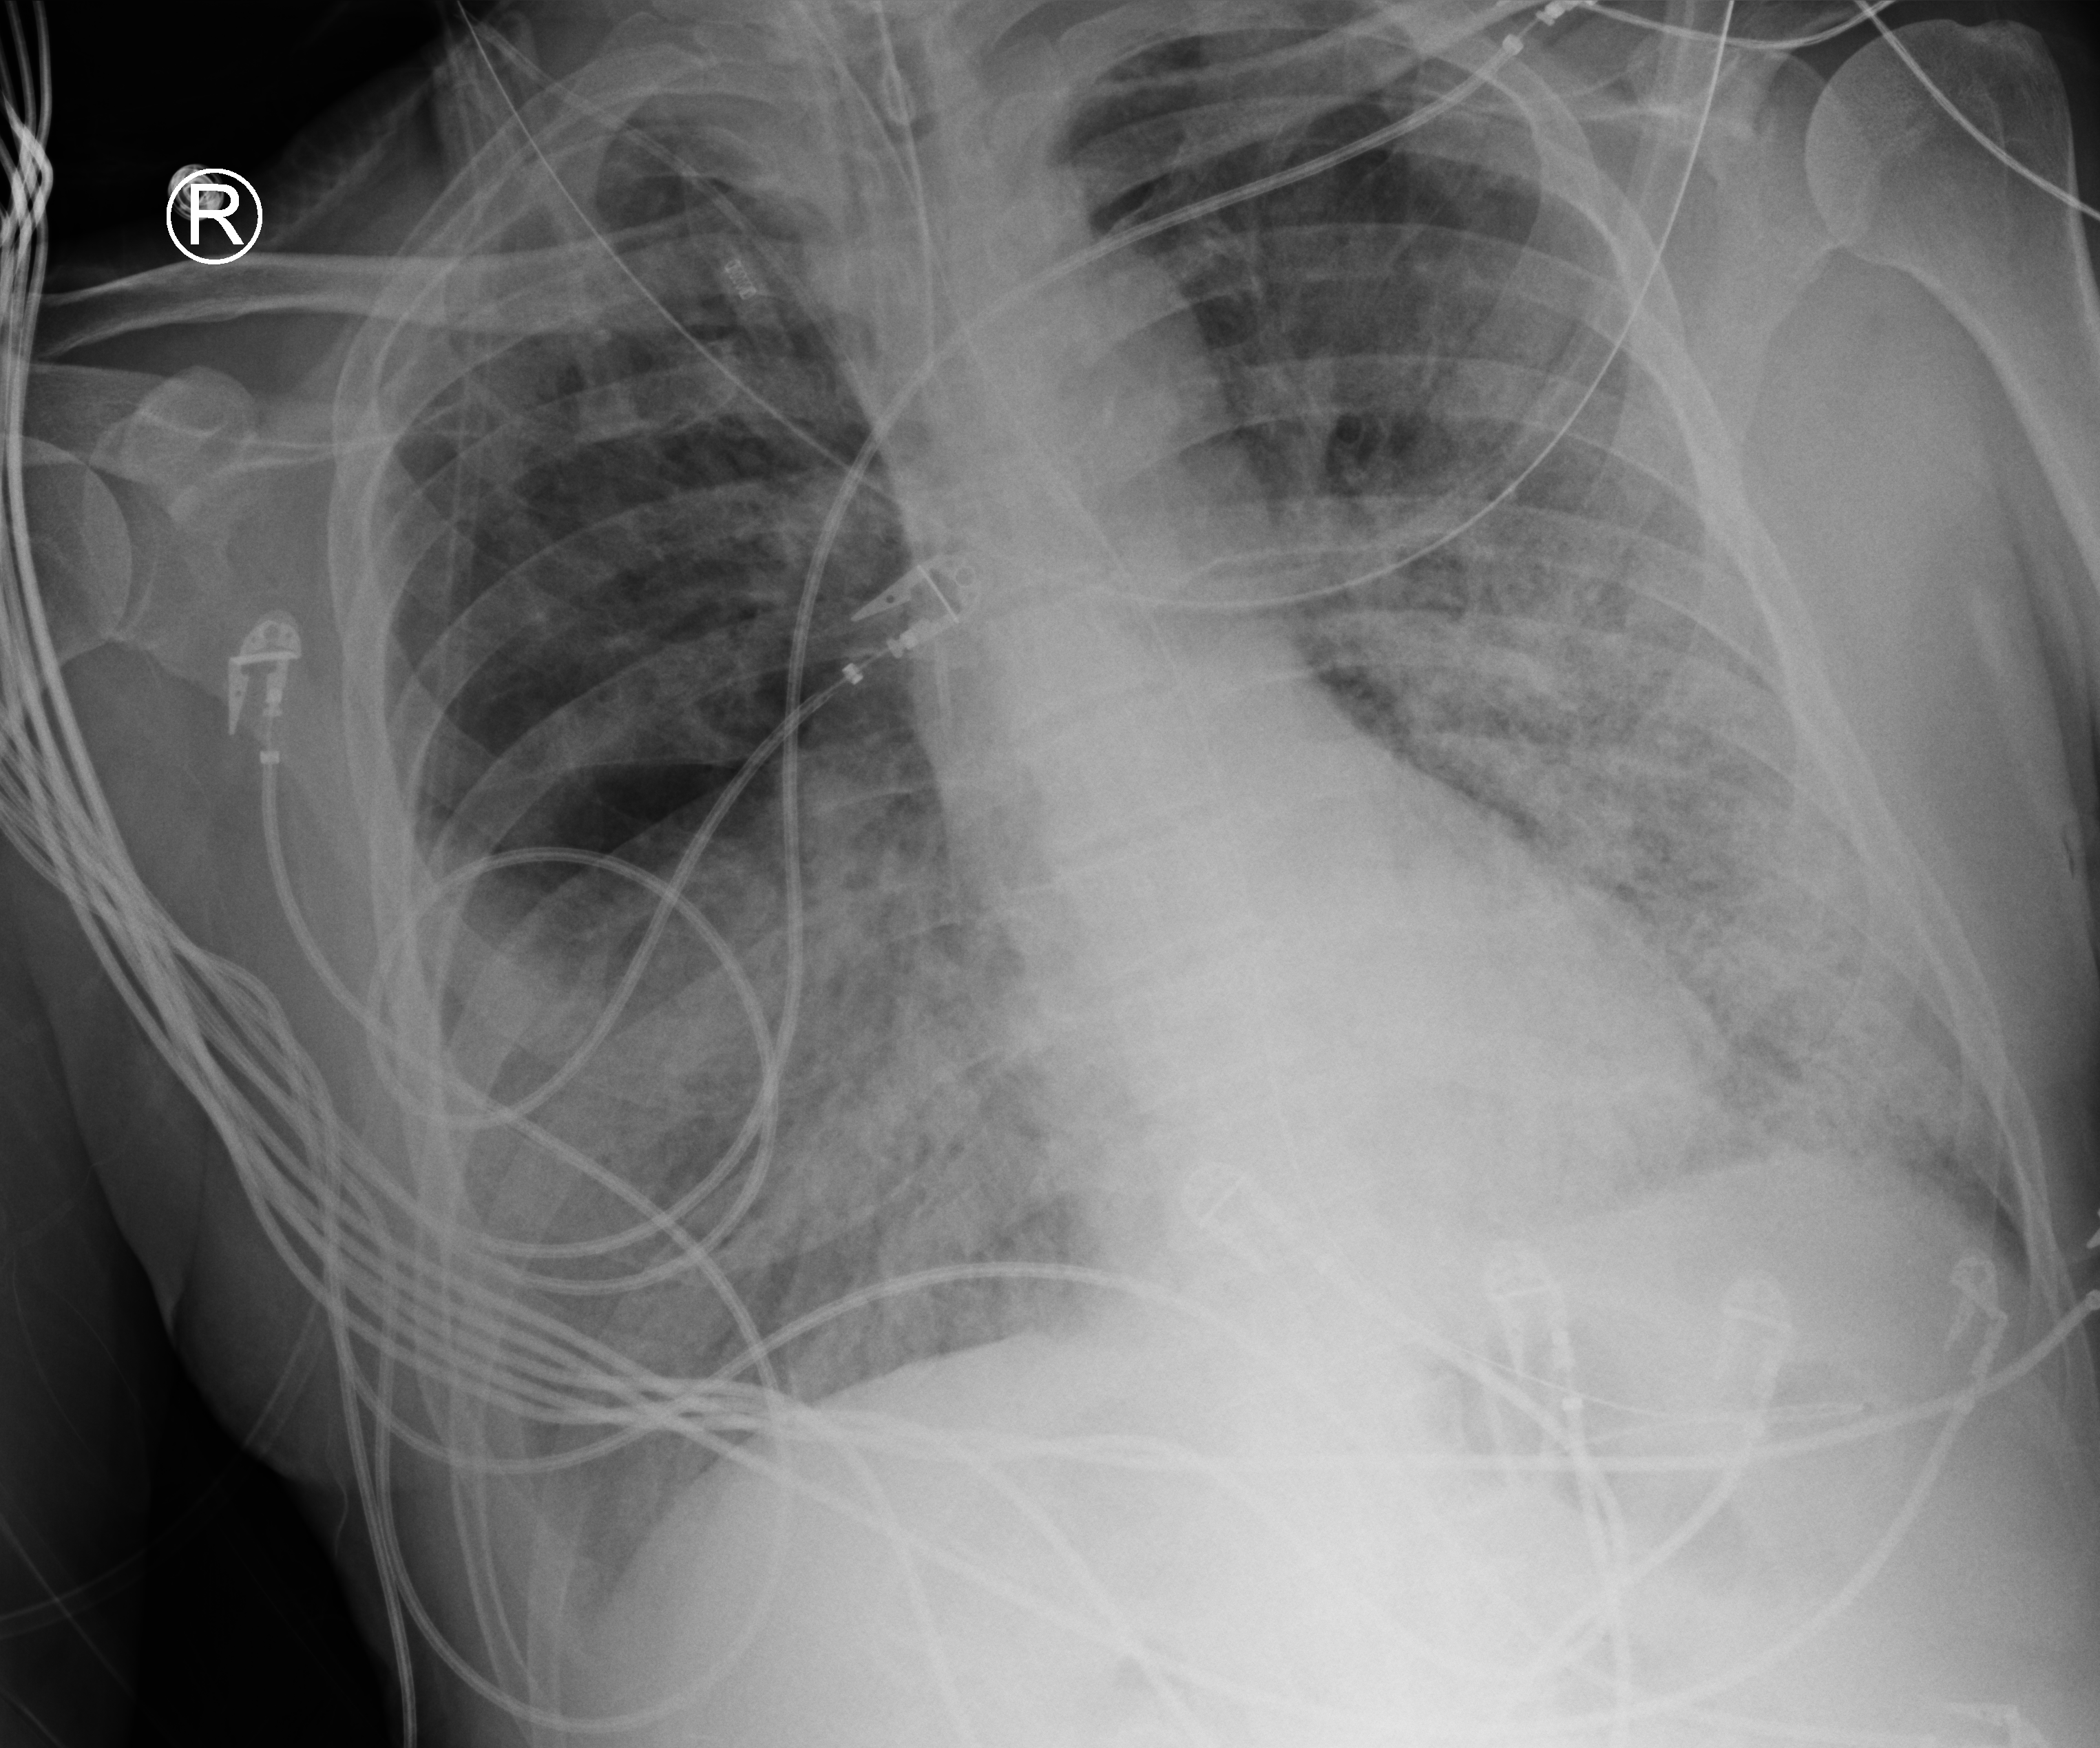
Bedside chest radiograph (computed radiography); anteroposterior (AP) projection. Male patient hospitalised with COVID-19, age 60–74 years.
From the hospital-stay record, not from the radiograph (when in the stay this image was taken is not recorded): other chronic lung disease (admission record): no; COPD (admission record): no; mechanically ventilated during this hospital stay: yes.